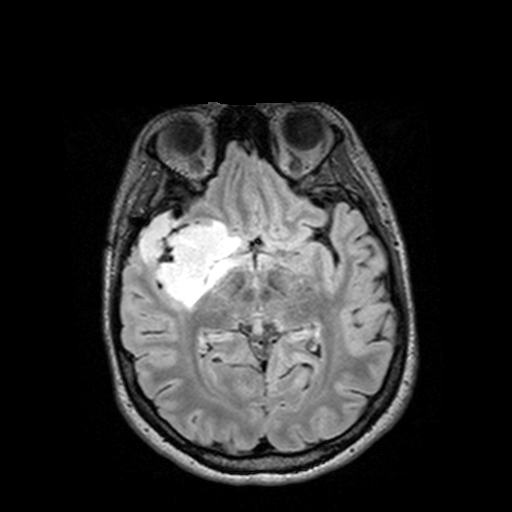
Brain MRI from a brain-tumour surgery series, one axial slice; slice 78 of 144 in the series (ordered by position); T2 FLAIR; 1 mm slice thickness; 512 × 512 image matrix, field of view 250 × 250 mm. From the clinical record (not read from this slice): histopathology: Astrocytoma; WHO grade: 3; IDH mutation: yes; tumour location: Right Insular Temporal.
Annotated regions visible in this slice (expert manual segmentation):
- tumour: bounding box (x1, y1, x2, y2) in pixels: (126, 215, 232, 307)